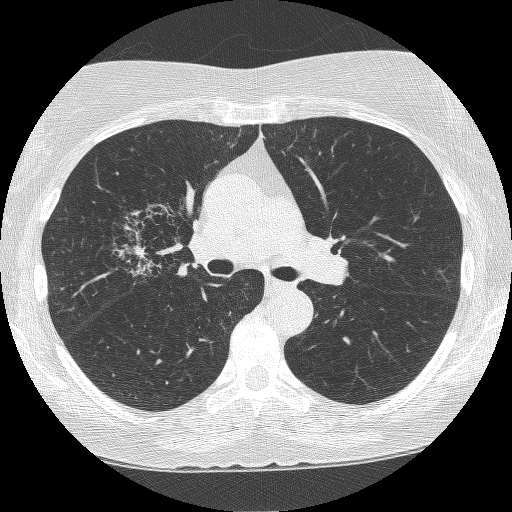
Chest CT (low-dose screening protocol), one axial image, second screening round (one year after baseline), lung window (W 1500 / L -600 HU), lung (sharp) reconstruction kernel (BONE), slice 150 of 249 in the series. Female participant, aged 64 years at enrolment. Former smoker at enrolment.
Lesion marked by an expert reader, bounding box [x1, y1, x2, y2] px = [116, 205, 205, 289]. The screening reader recorded 4 non-calcified nodules or masses ≥4 mm on this exam; which of them this box marks is not recorded.